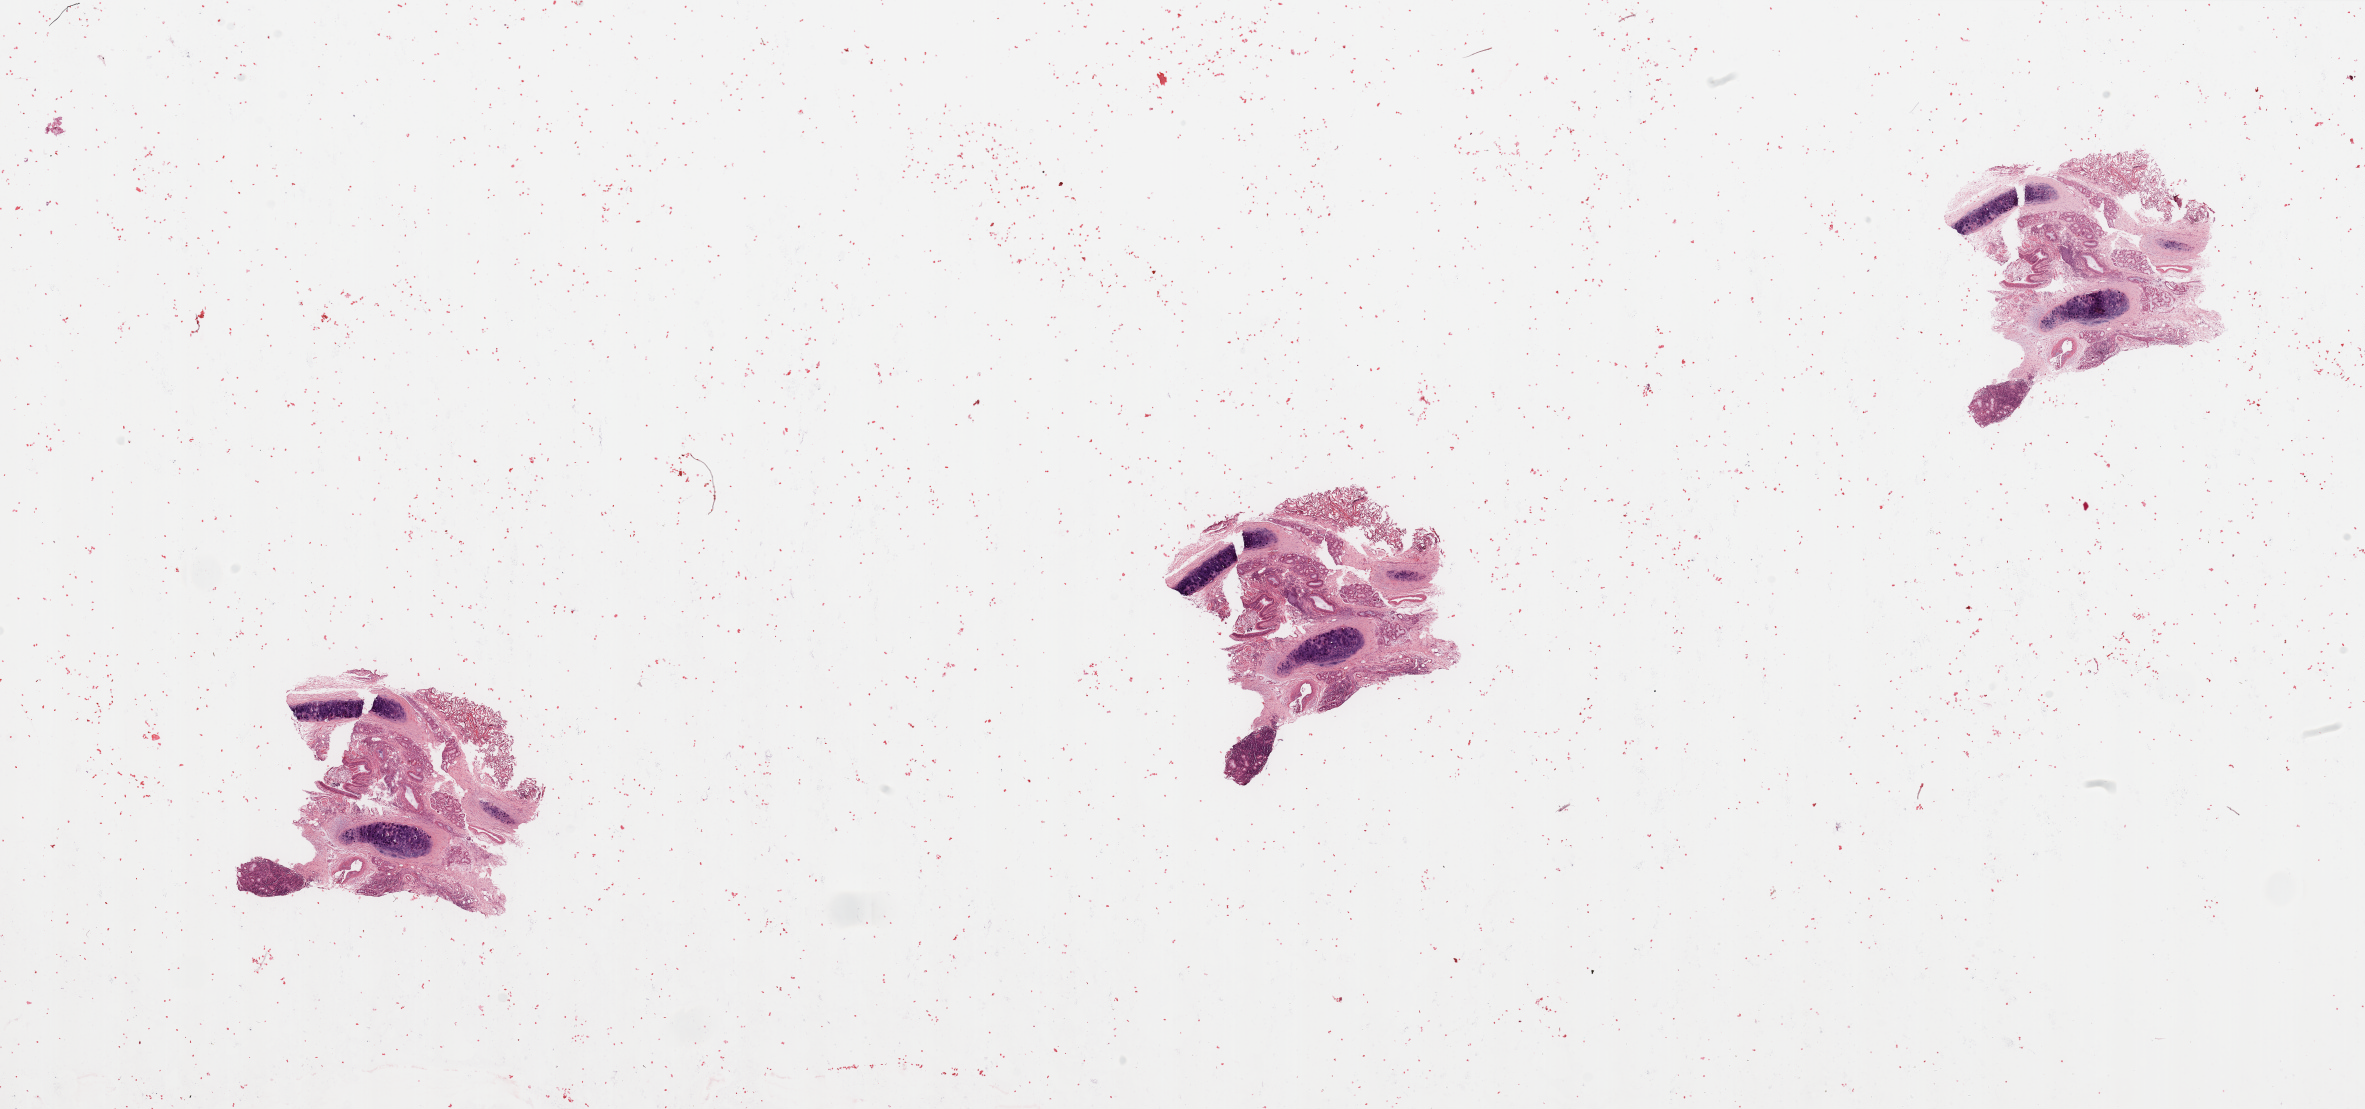
H&E-stained whole-slide image — whole scanned area (about 37.4 x 17.5 mm, acquisition: 20x scan) shown as a low-resolution overview; normal (non-tumour) tissue sample, sampled site: lung. Patient: female, age 63 years.
This section: normal (non-tumour) tissue from the same patient. Patient diagnosis: Adenocarcinoma, NOS.